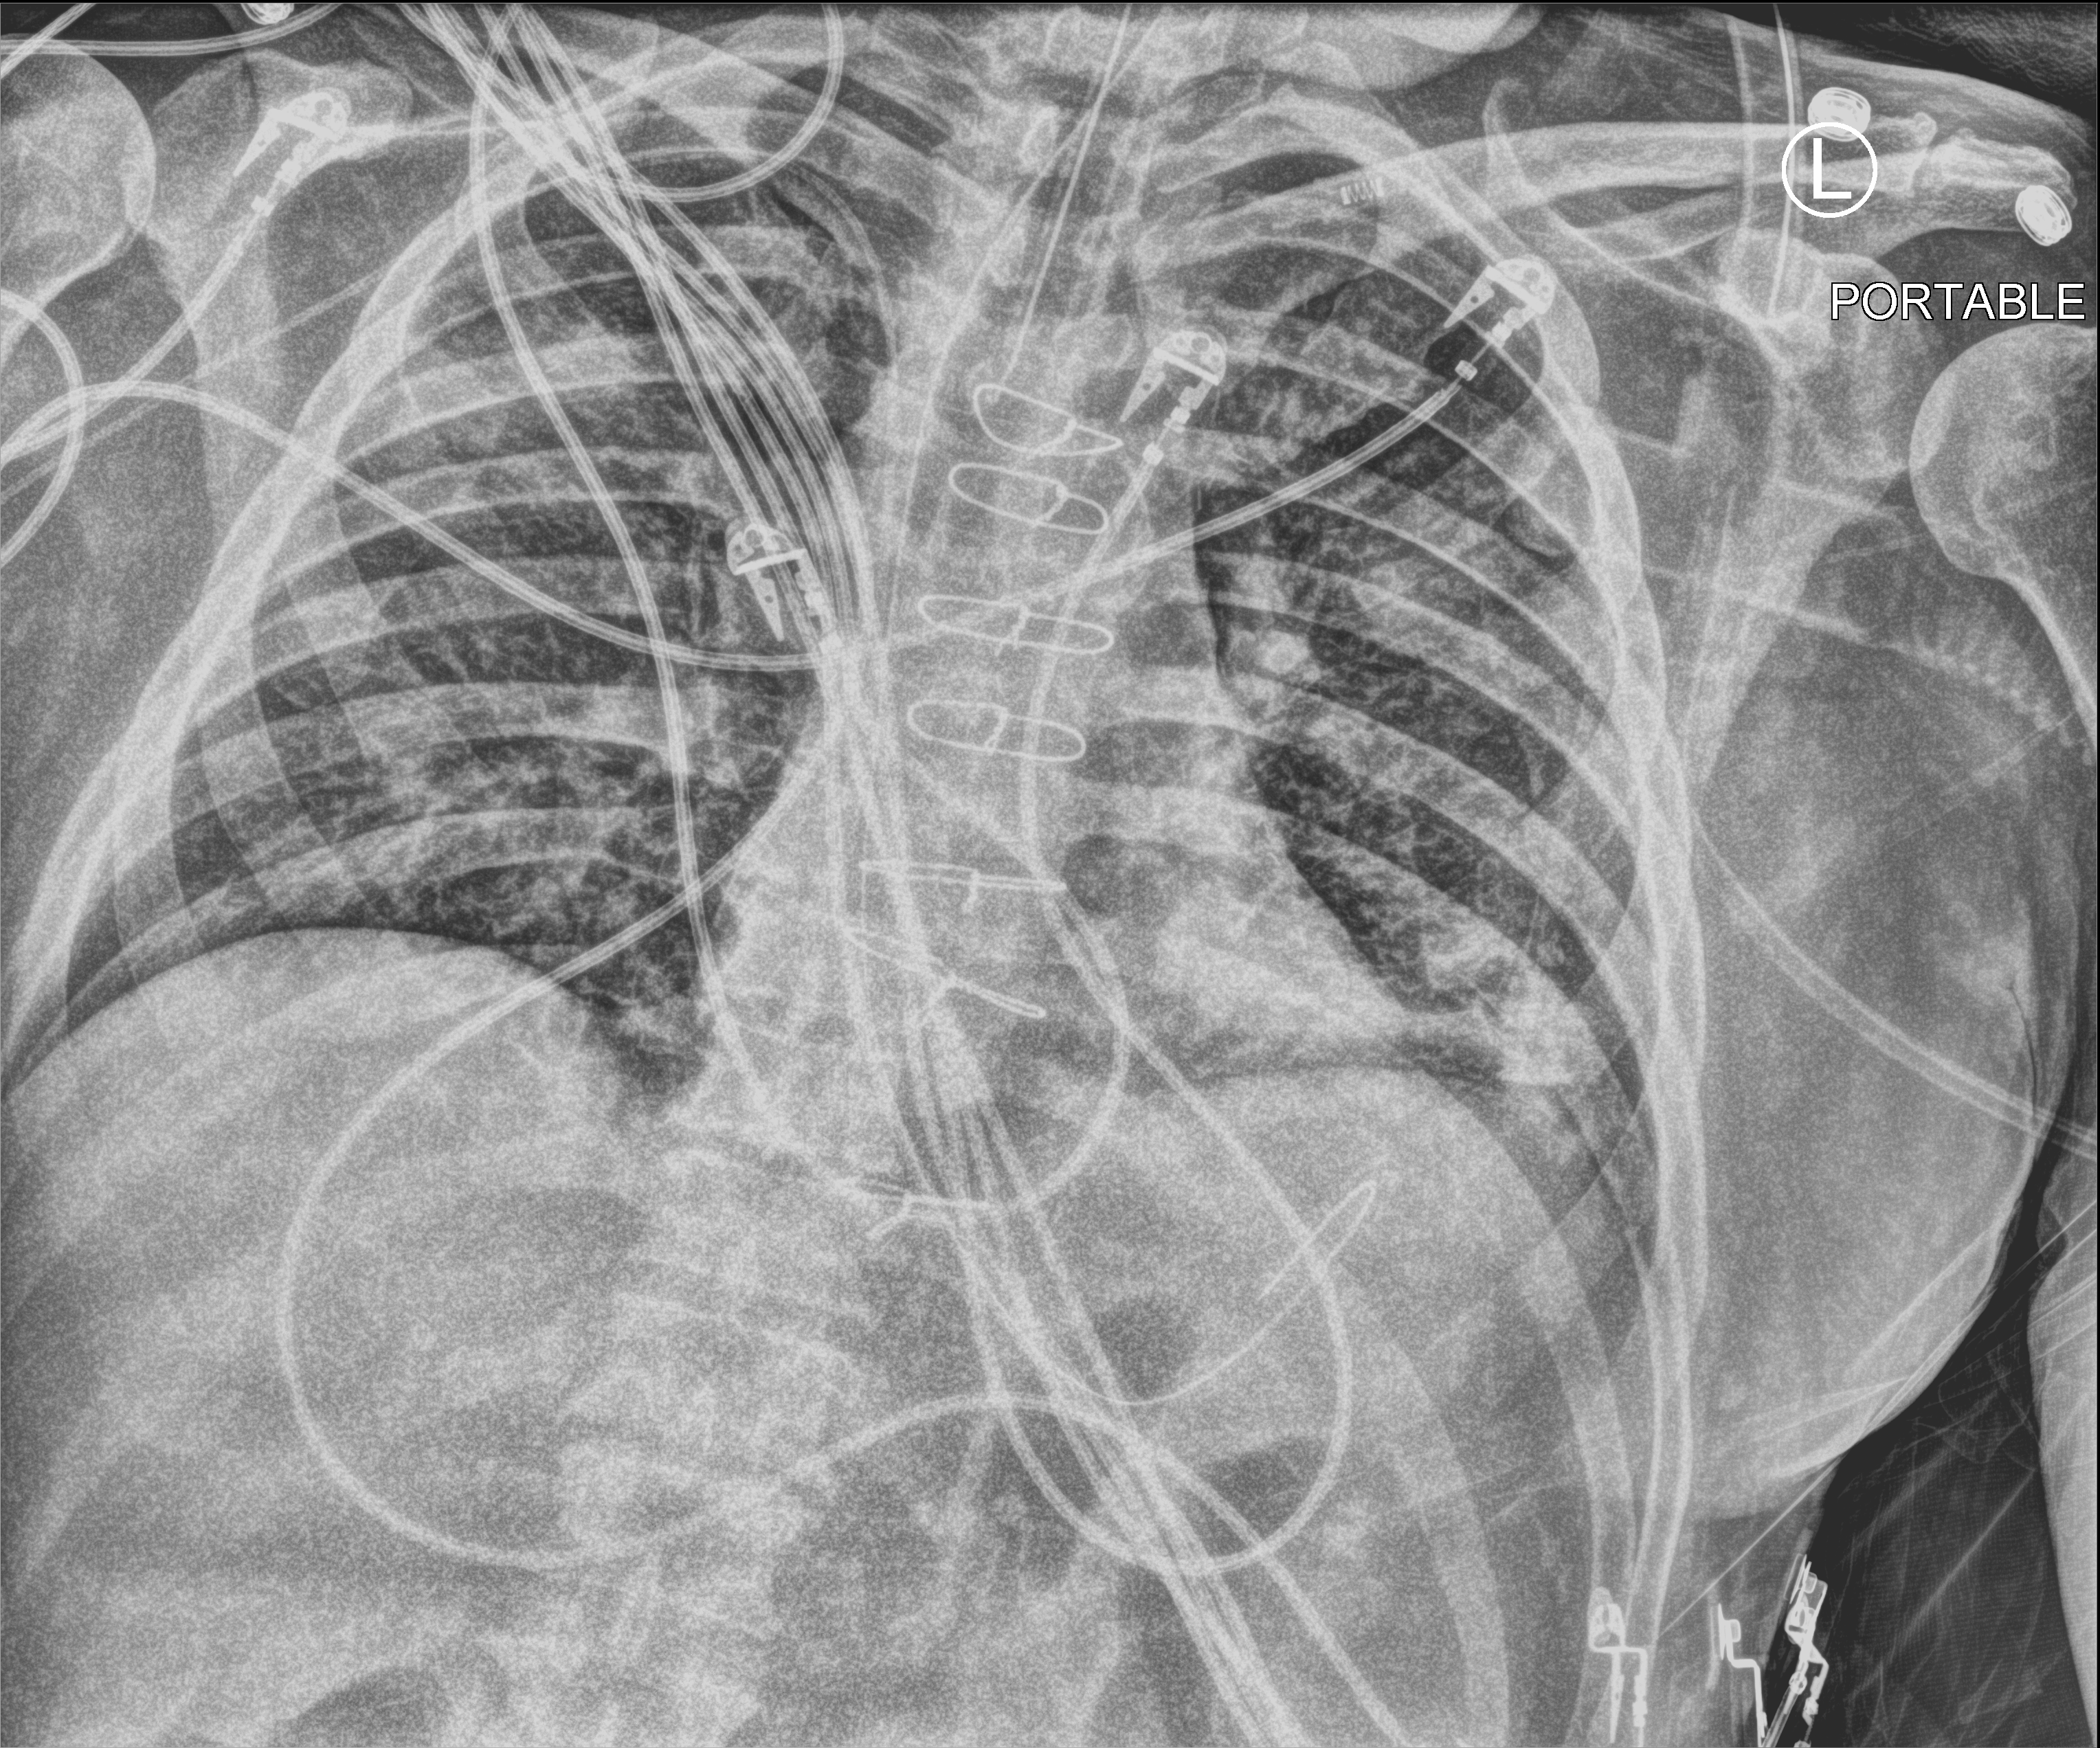
Portable chest radiograph; anteroposterior (AP) projection. Male patient hospitalised with COVID-19, age 60–74 years.
From the hospital-stay record, not from the radiograph (when in the stay this image was taken is not recorded): mechanically ventilated during this hospital stay: yes.